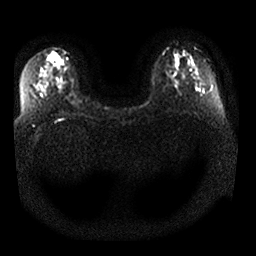
Breast MRI, one axial slice. Position 15 of 25 along the scan axis. Diffusion-weighted series; image 2 of 4 stored at this slice position (different b-values; order by instance number). 1.5 T. 4 mm slice thickness. 256 × 256 image matrix, field of view 340 × 340 mm. Female patient.
Annotated regions visible in this slice (outlined manually by an expert reader):
- tumour on diffusion-weighted imaging: bounding box [x1, y1, x2, y2] px = [48, 52, 63, 66]